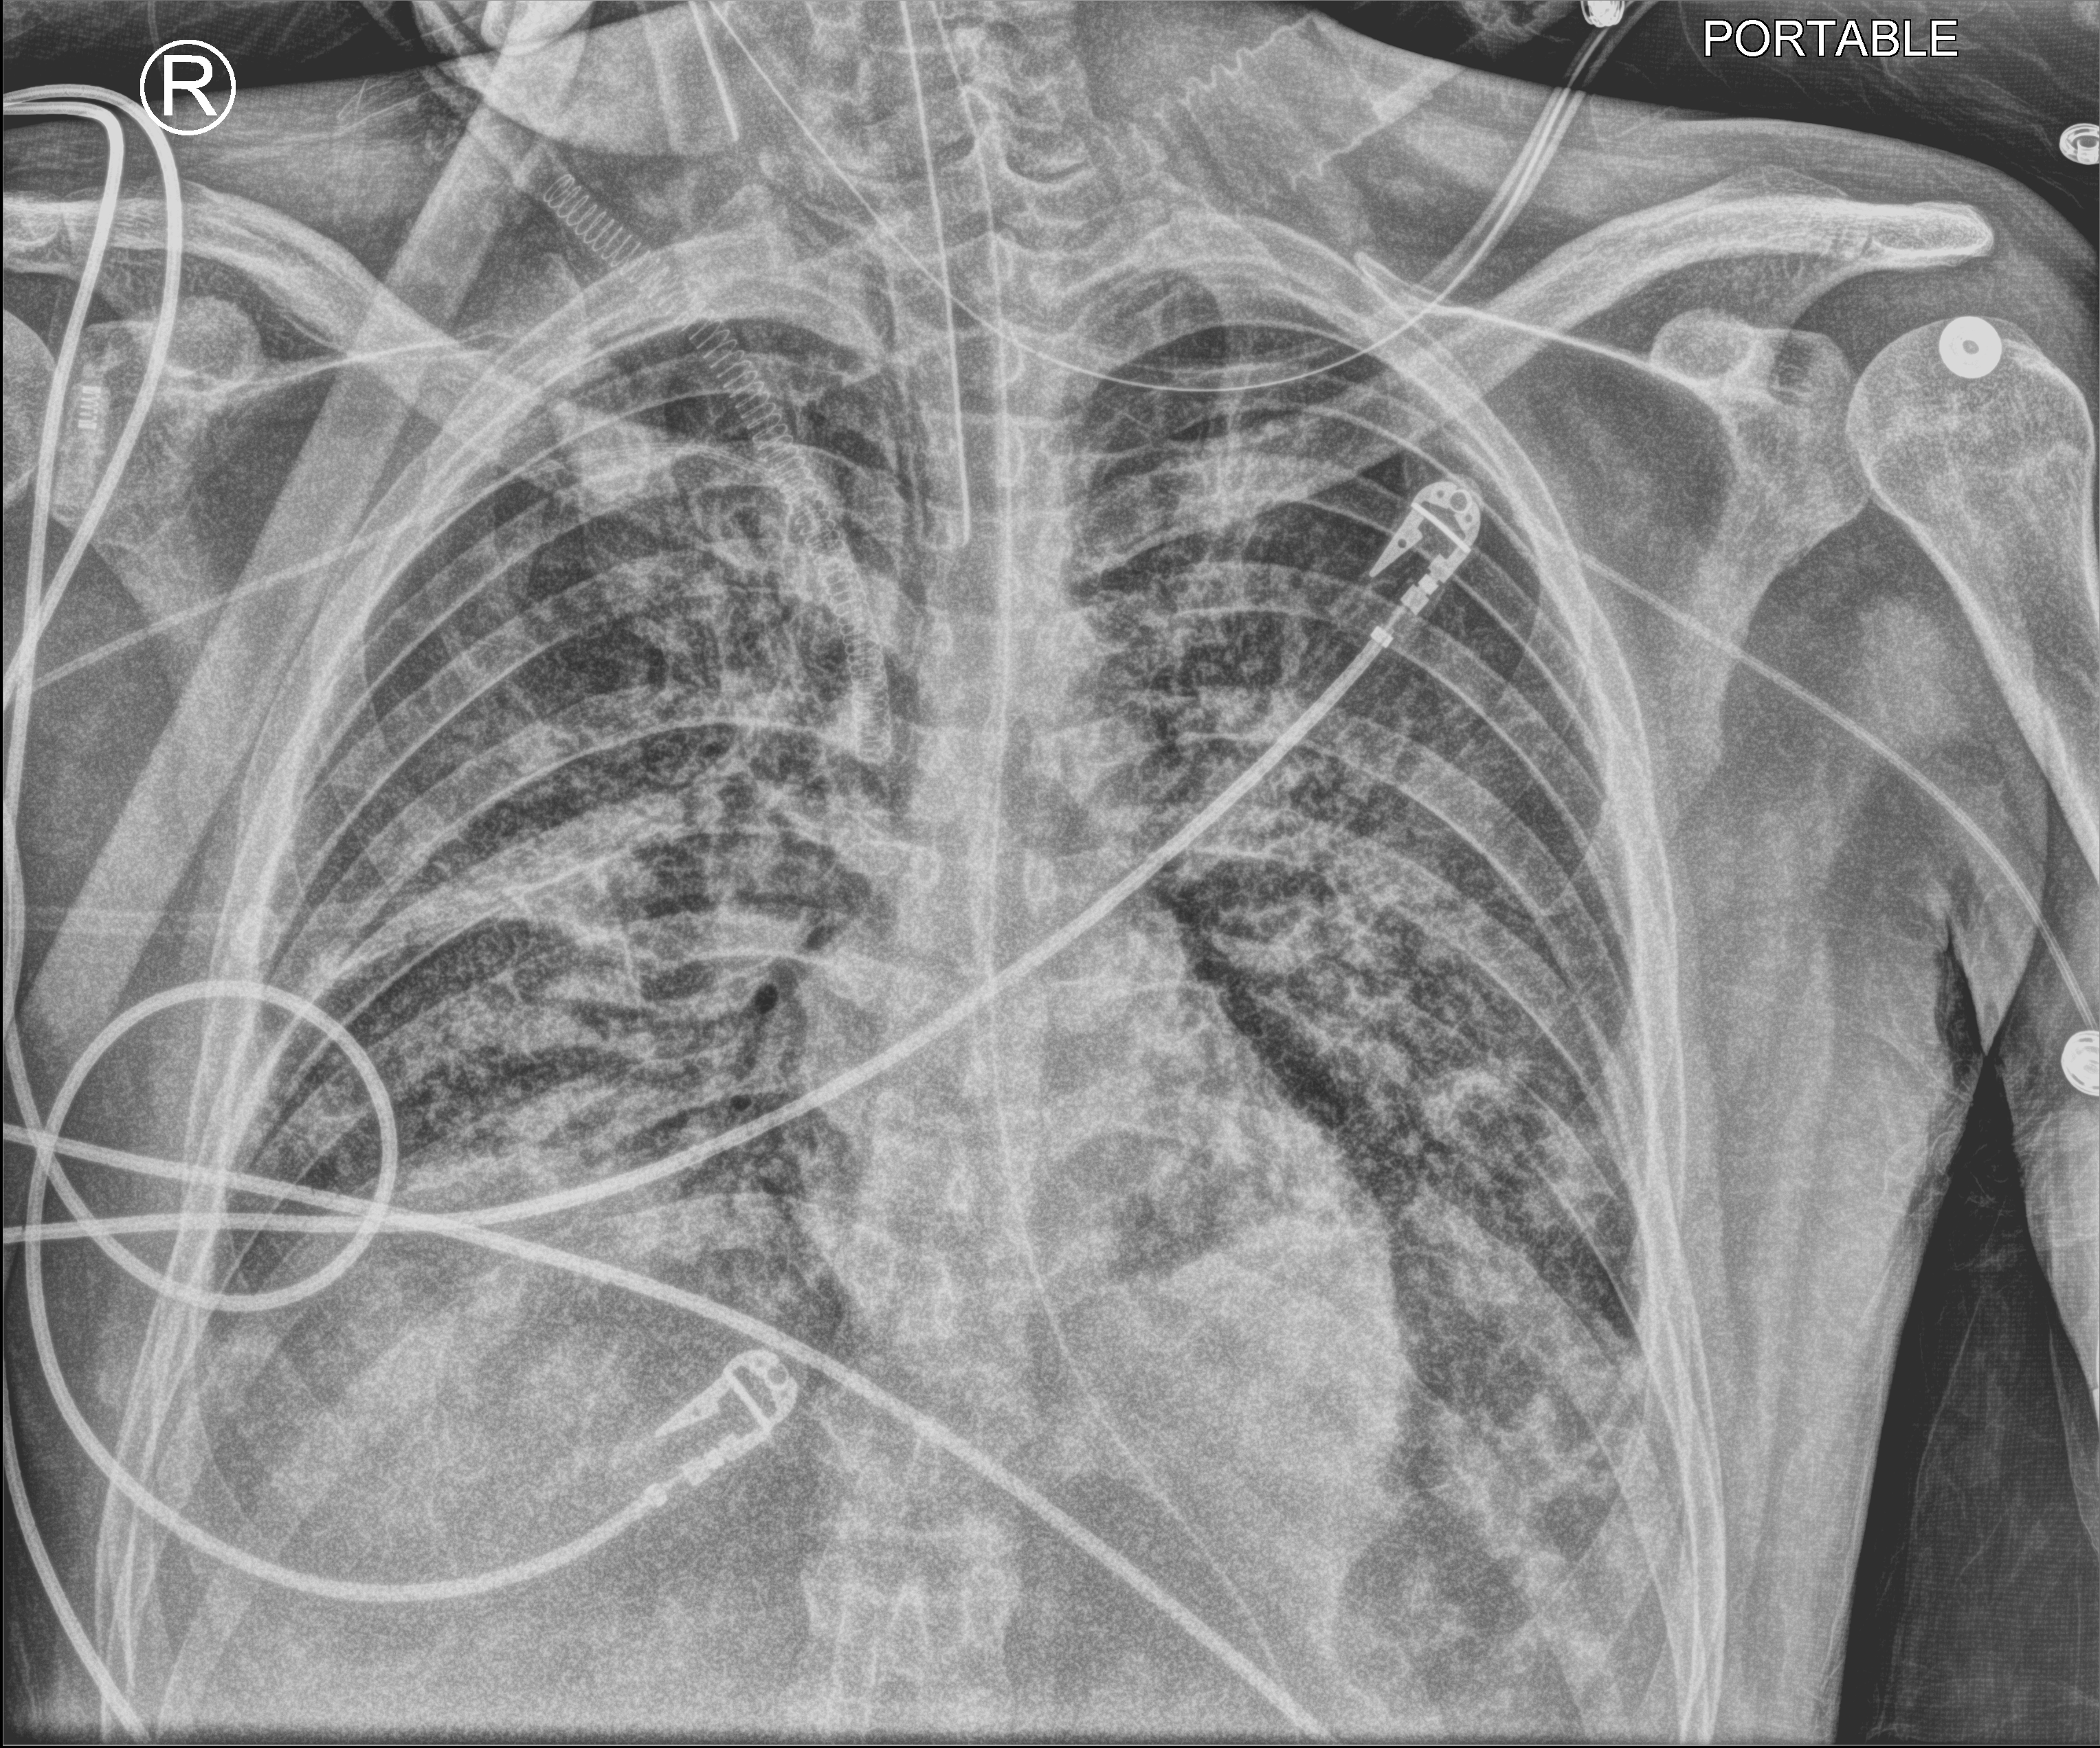
Portable chest radiograph, anteroposterior (AP) projection. Patient hospitalised with COVID-19, aged 18–59 years.
Hospital-stay facts (about this admission, not read from this image; timing relative to this image not recorded):
- admitted to intensive care during this hospital stay: yes
- chronic kidney disease (admission record): no
- mechanically ventilated during this hospital stay: yes